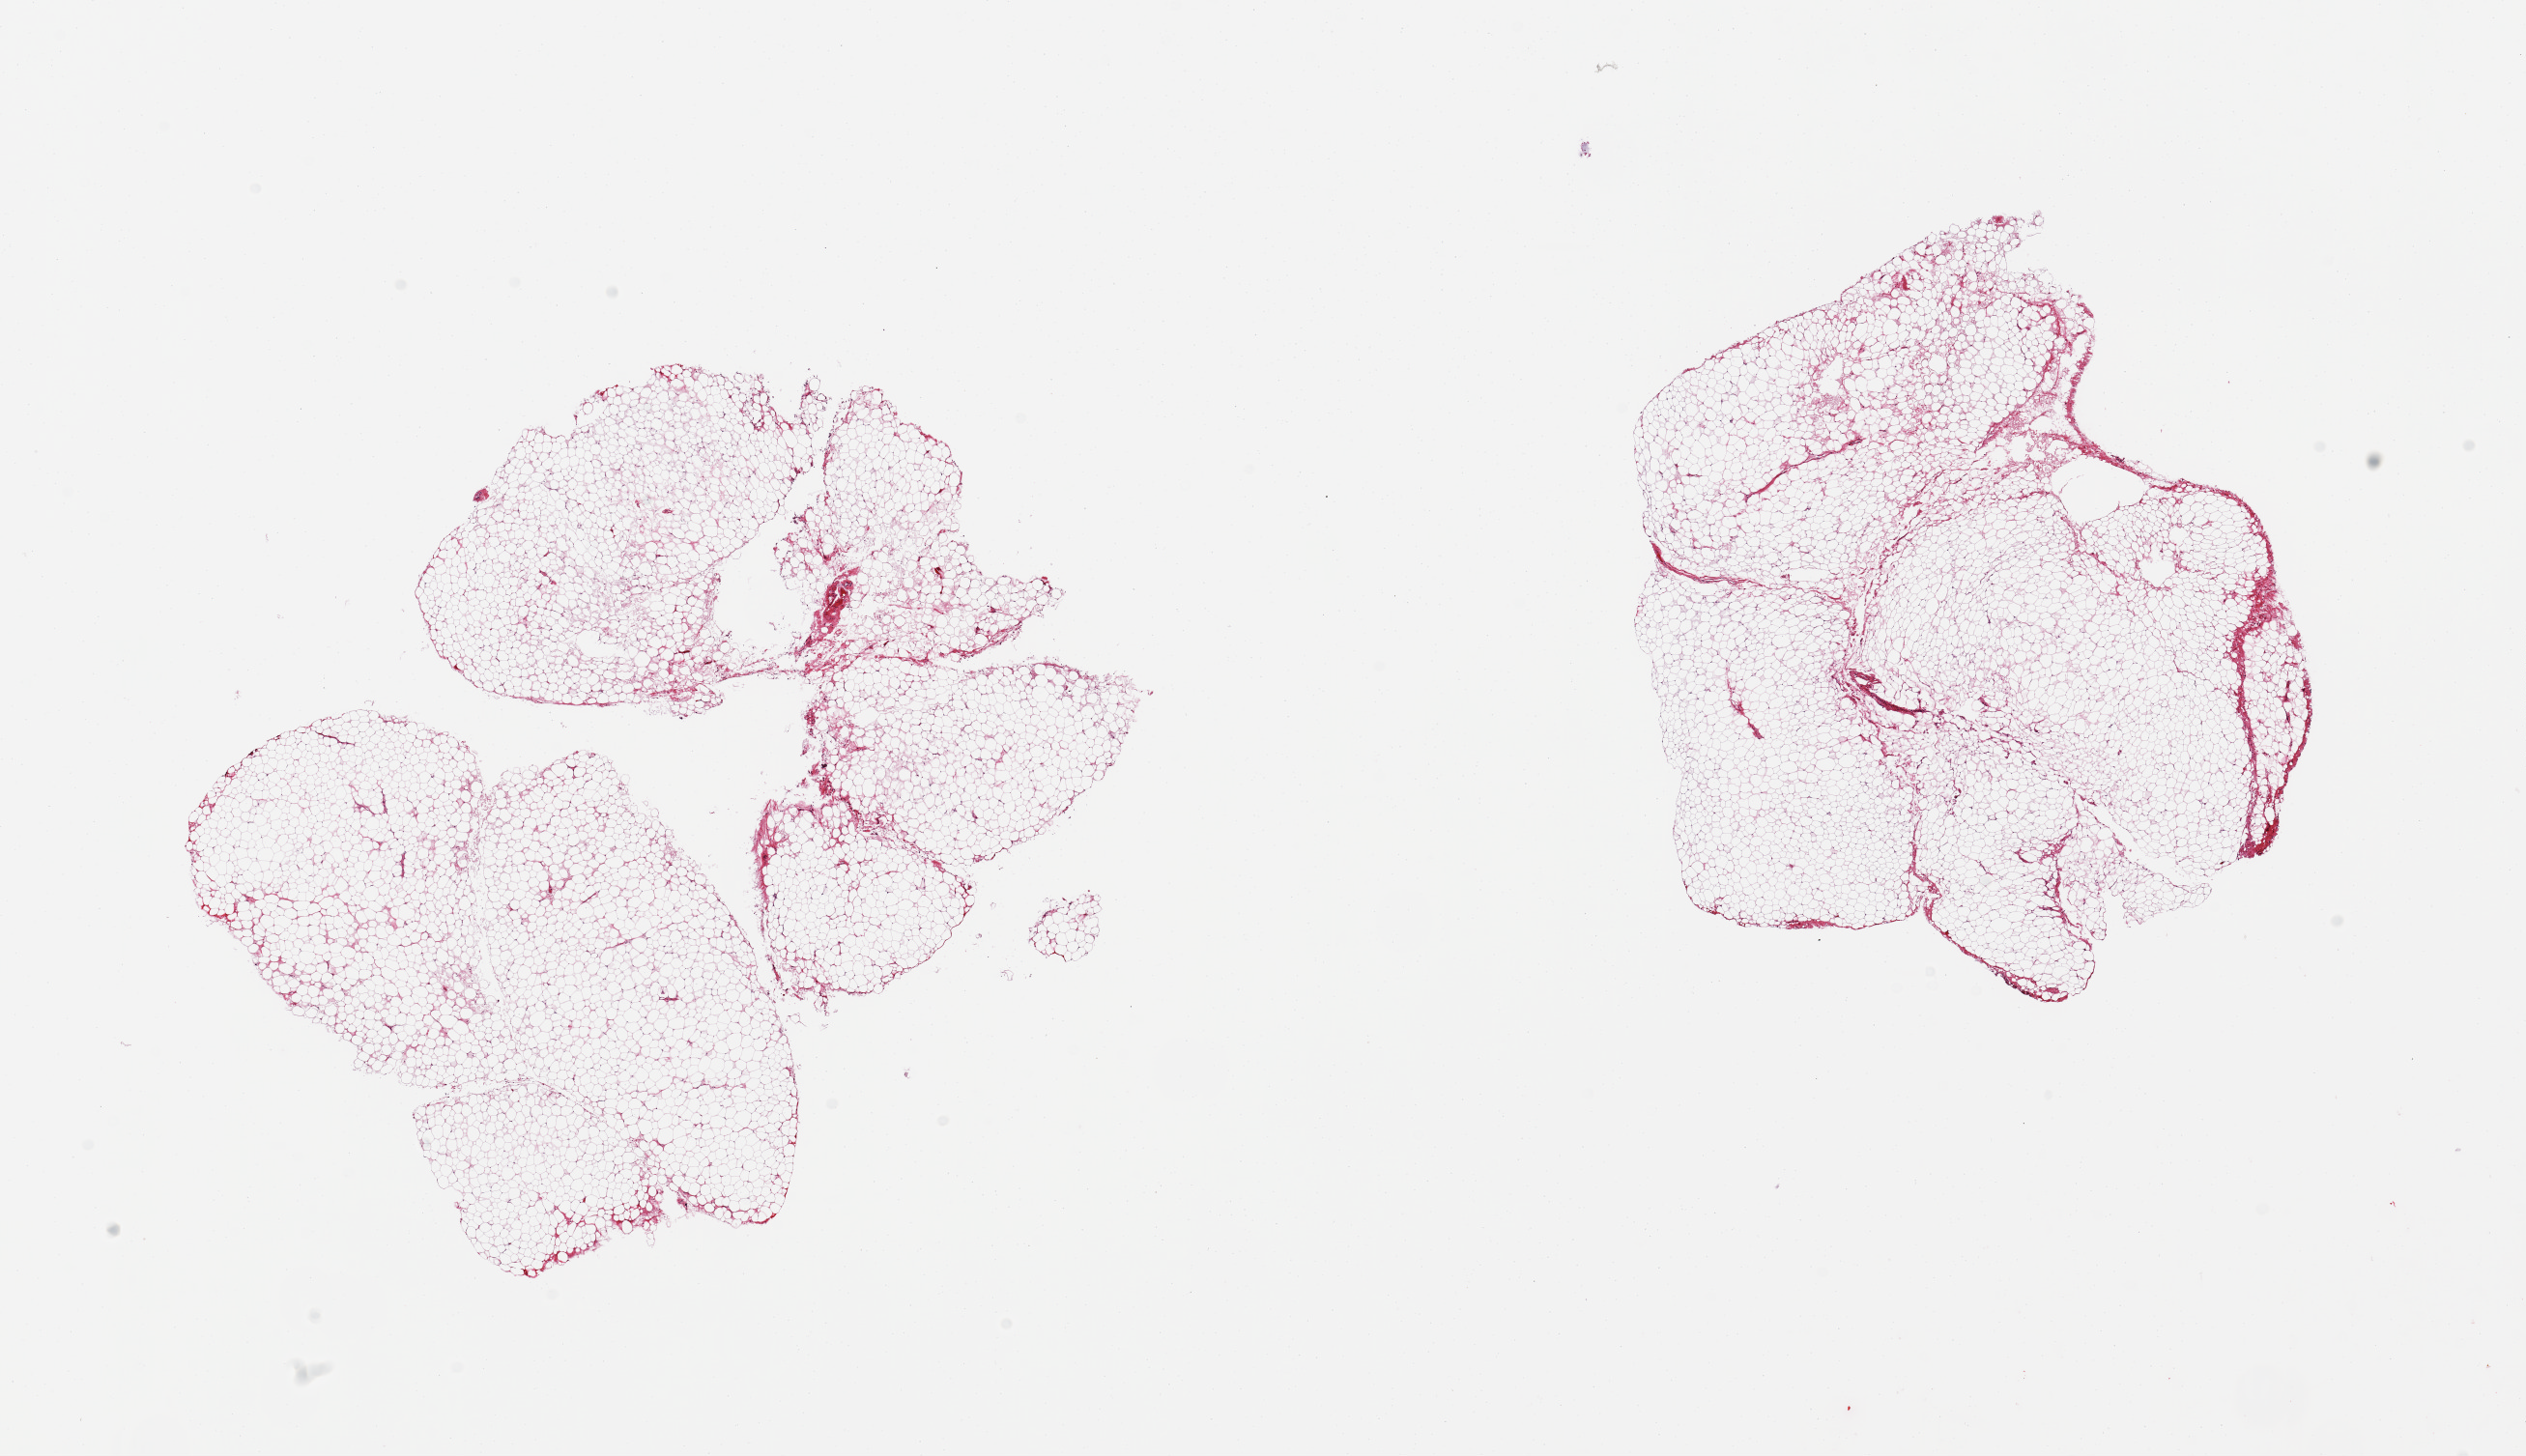
Whole-slide image, H&E stain, low-resolution overview of the scanned area, about 20.7 x 11.9 mm, PAXgene-fixed paraffin-embedded (PFPE) section, section of adrenal gland (target tissue), tissue donor sample. Donor: male.
Pathologist's review note for this sample: 2 pieces; fat only.